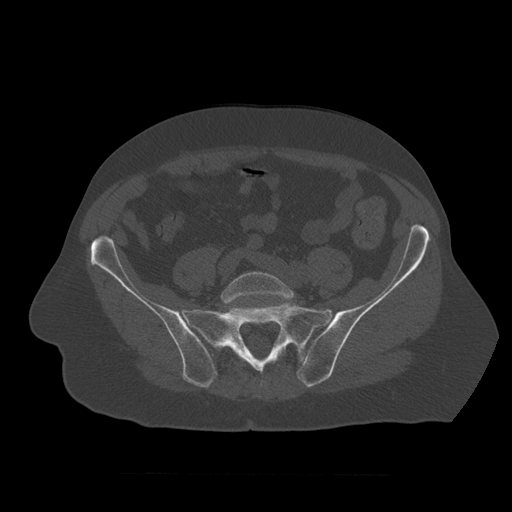
CT including the spine, one axial slice. Position 240 of 450 along the scan axis. Reconstruction kernel STANDARD. 120 kVp. Bone window (W 1800 / L 400 HU). 512 × 512 image matrix, field of view 405 × 405 mm. Patient age 75 years. Case-level facts recorded for this patient, not image findings: primary cancer: prostate.
Structures marked on this image (semi-automatic segmentation, software-assisted and operator-edited):
- L5 vertebra: bounding box [x1, y1, x2, y2] px = [221, 272, 295, 304]